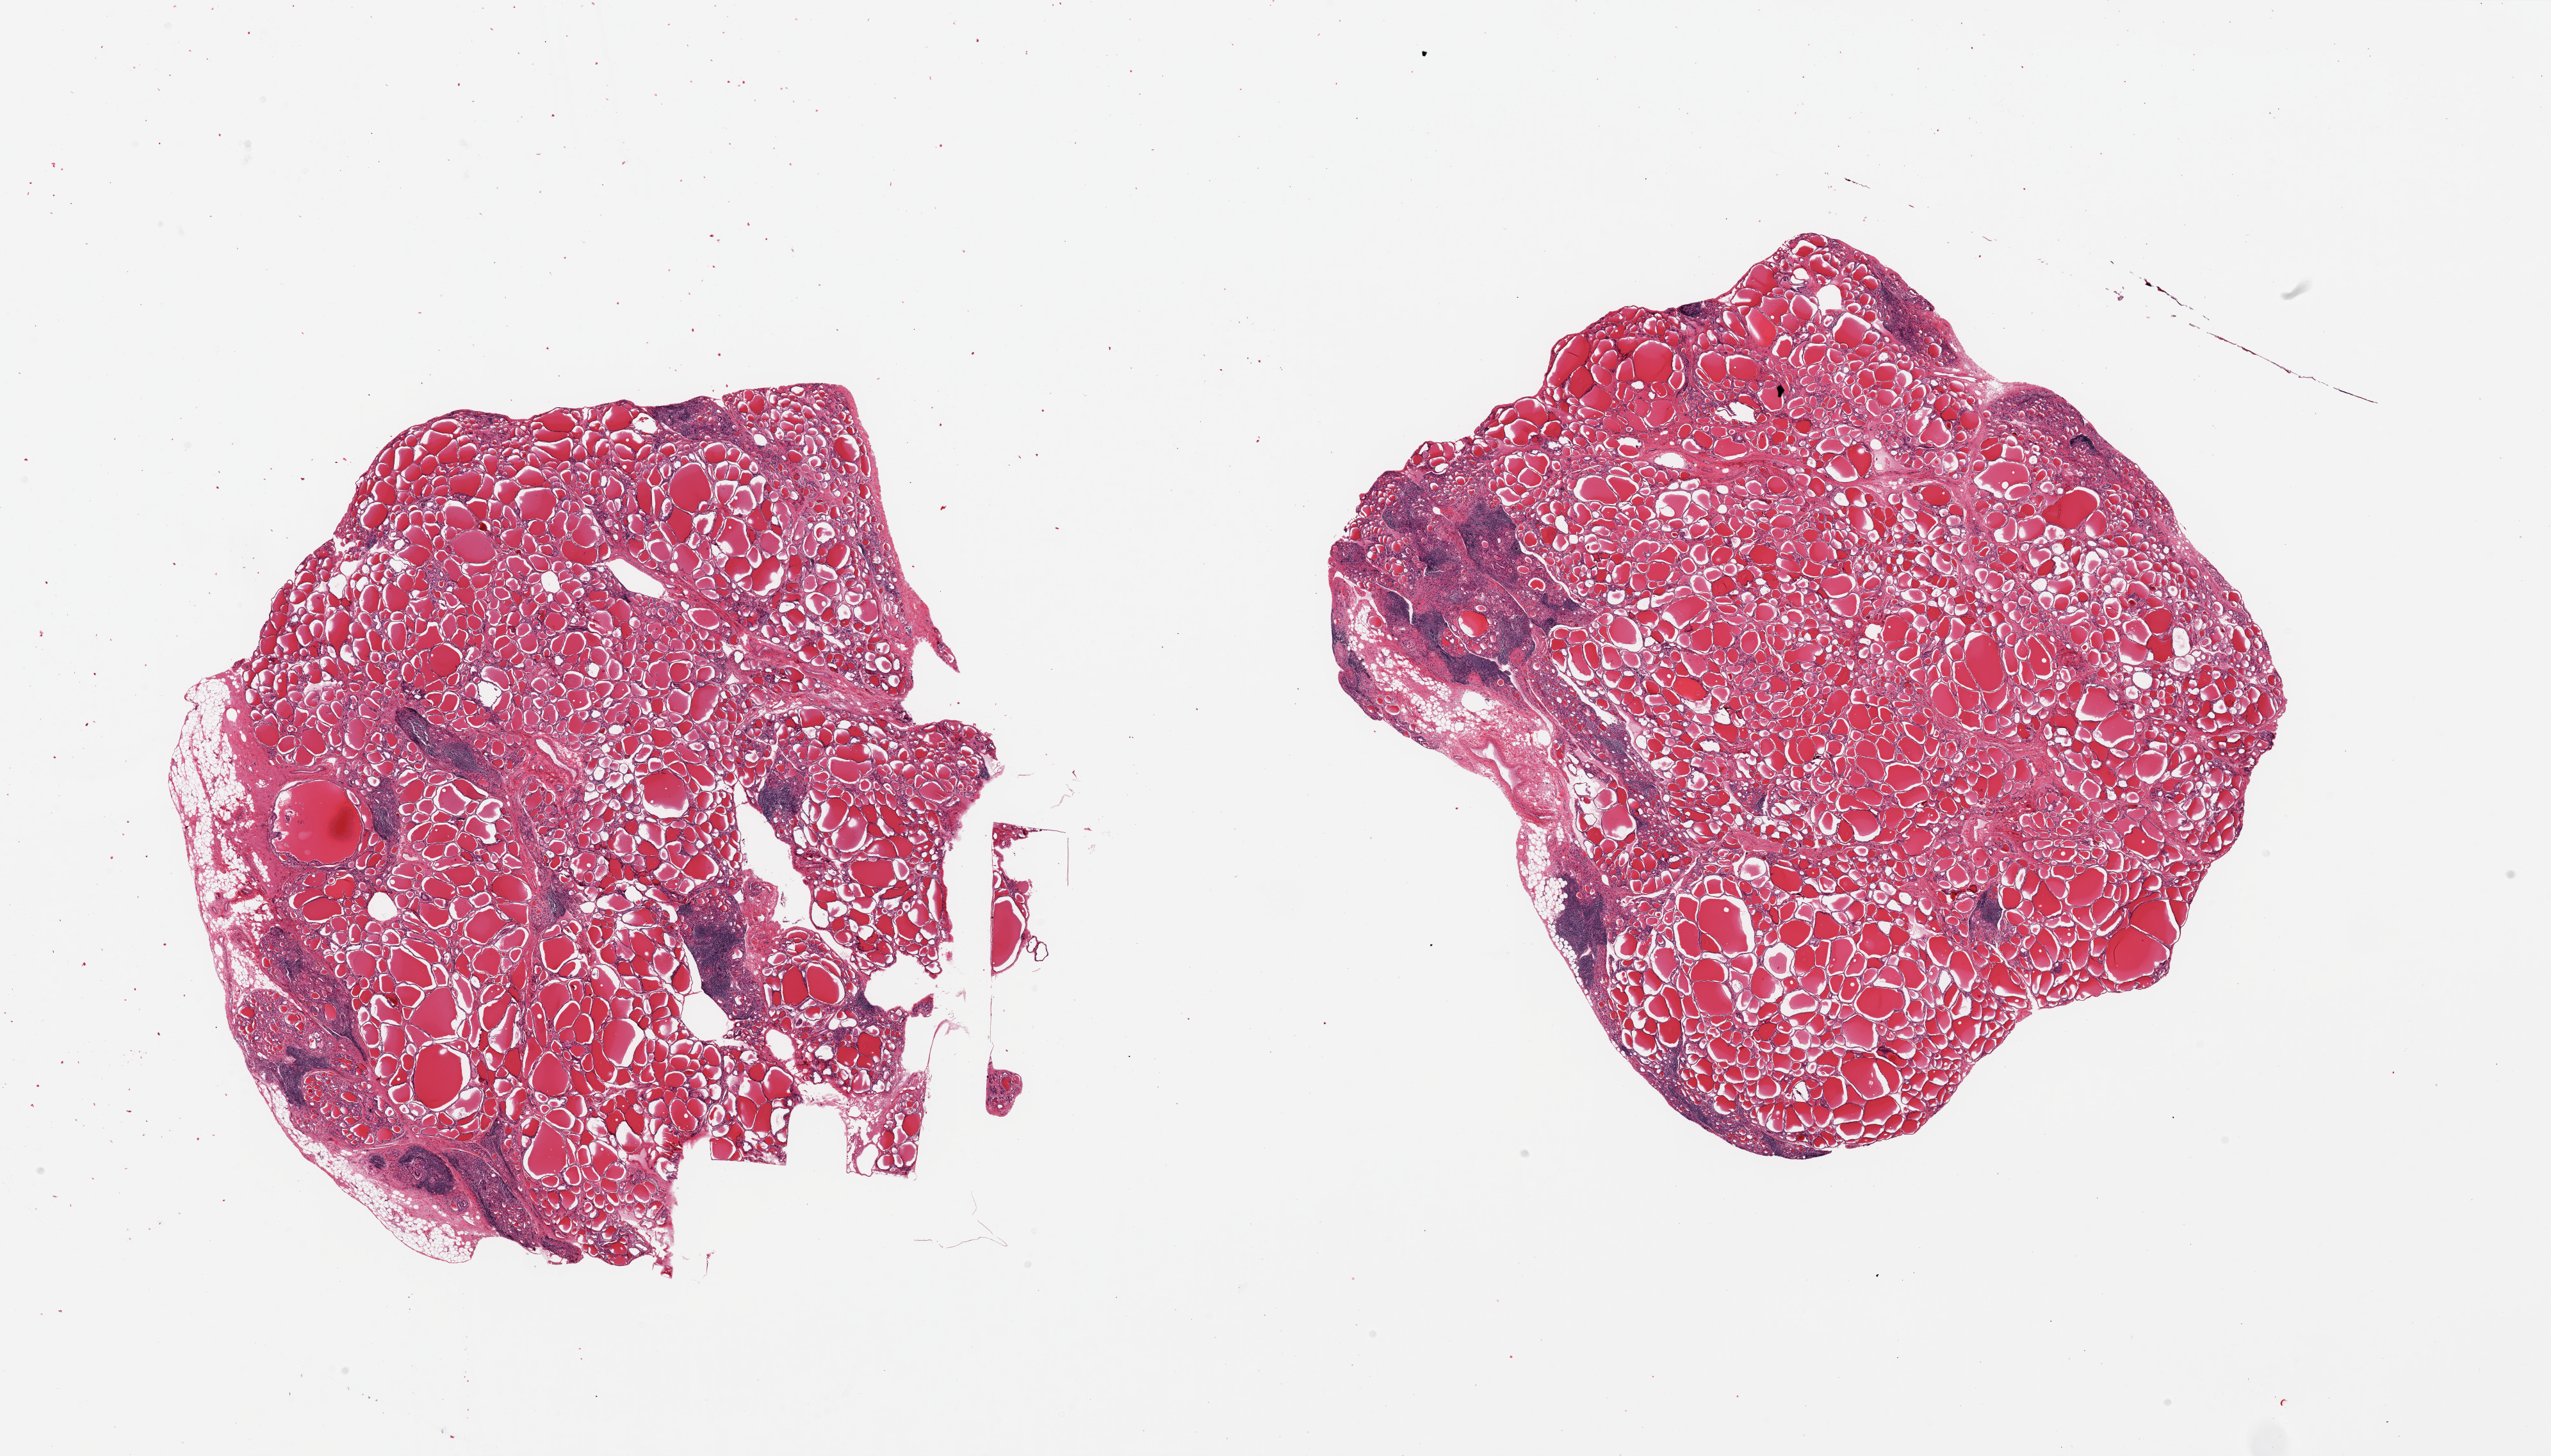
Haematoxylin and eosin whole-slide image, brightfield, whole scanned area (about 31.5 x 18.0 mm, from a 20x scan) shown as a low-resolution overview, PAXgene-fixed, paraffin-embedded tissue, sampled site (target tissue): thyroid, donor tissue sample. Donor sex: male.
- review note (as recorded): 2 pieces moderate Hashimoto lymphocytic thyroiditis